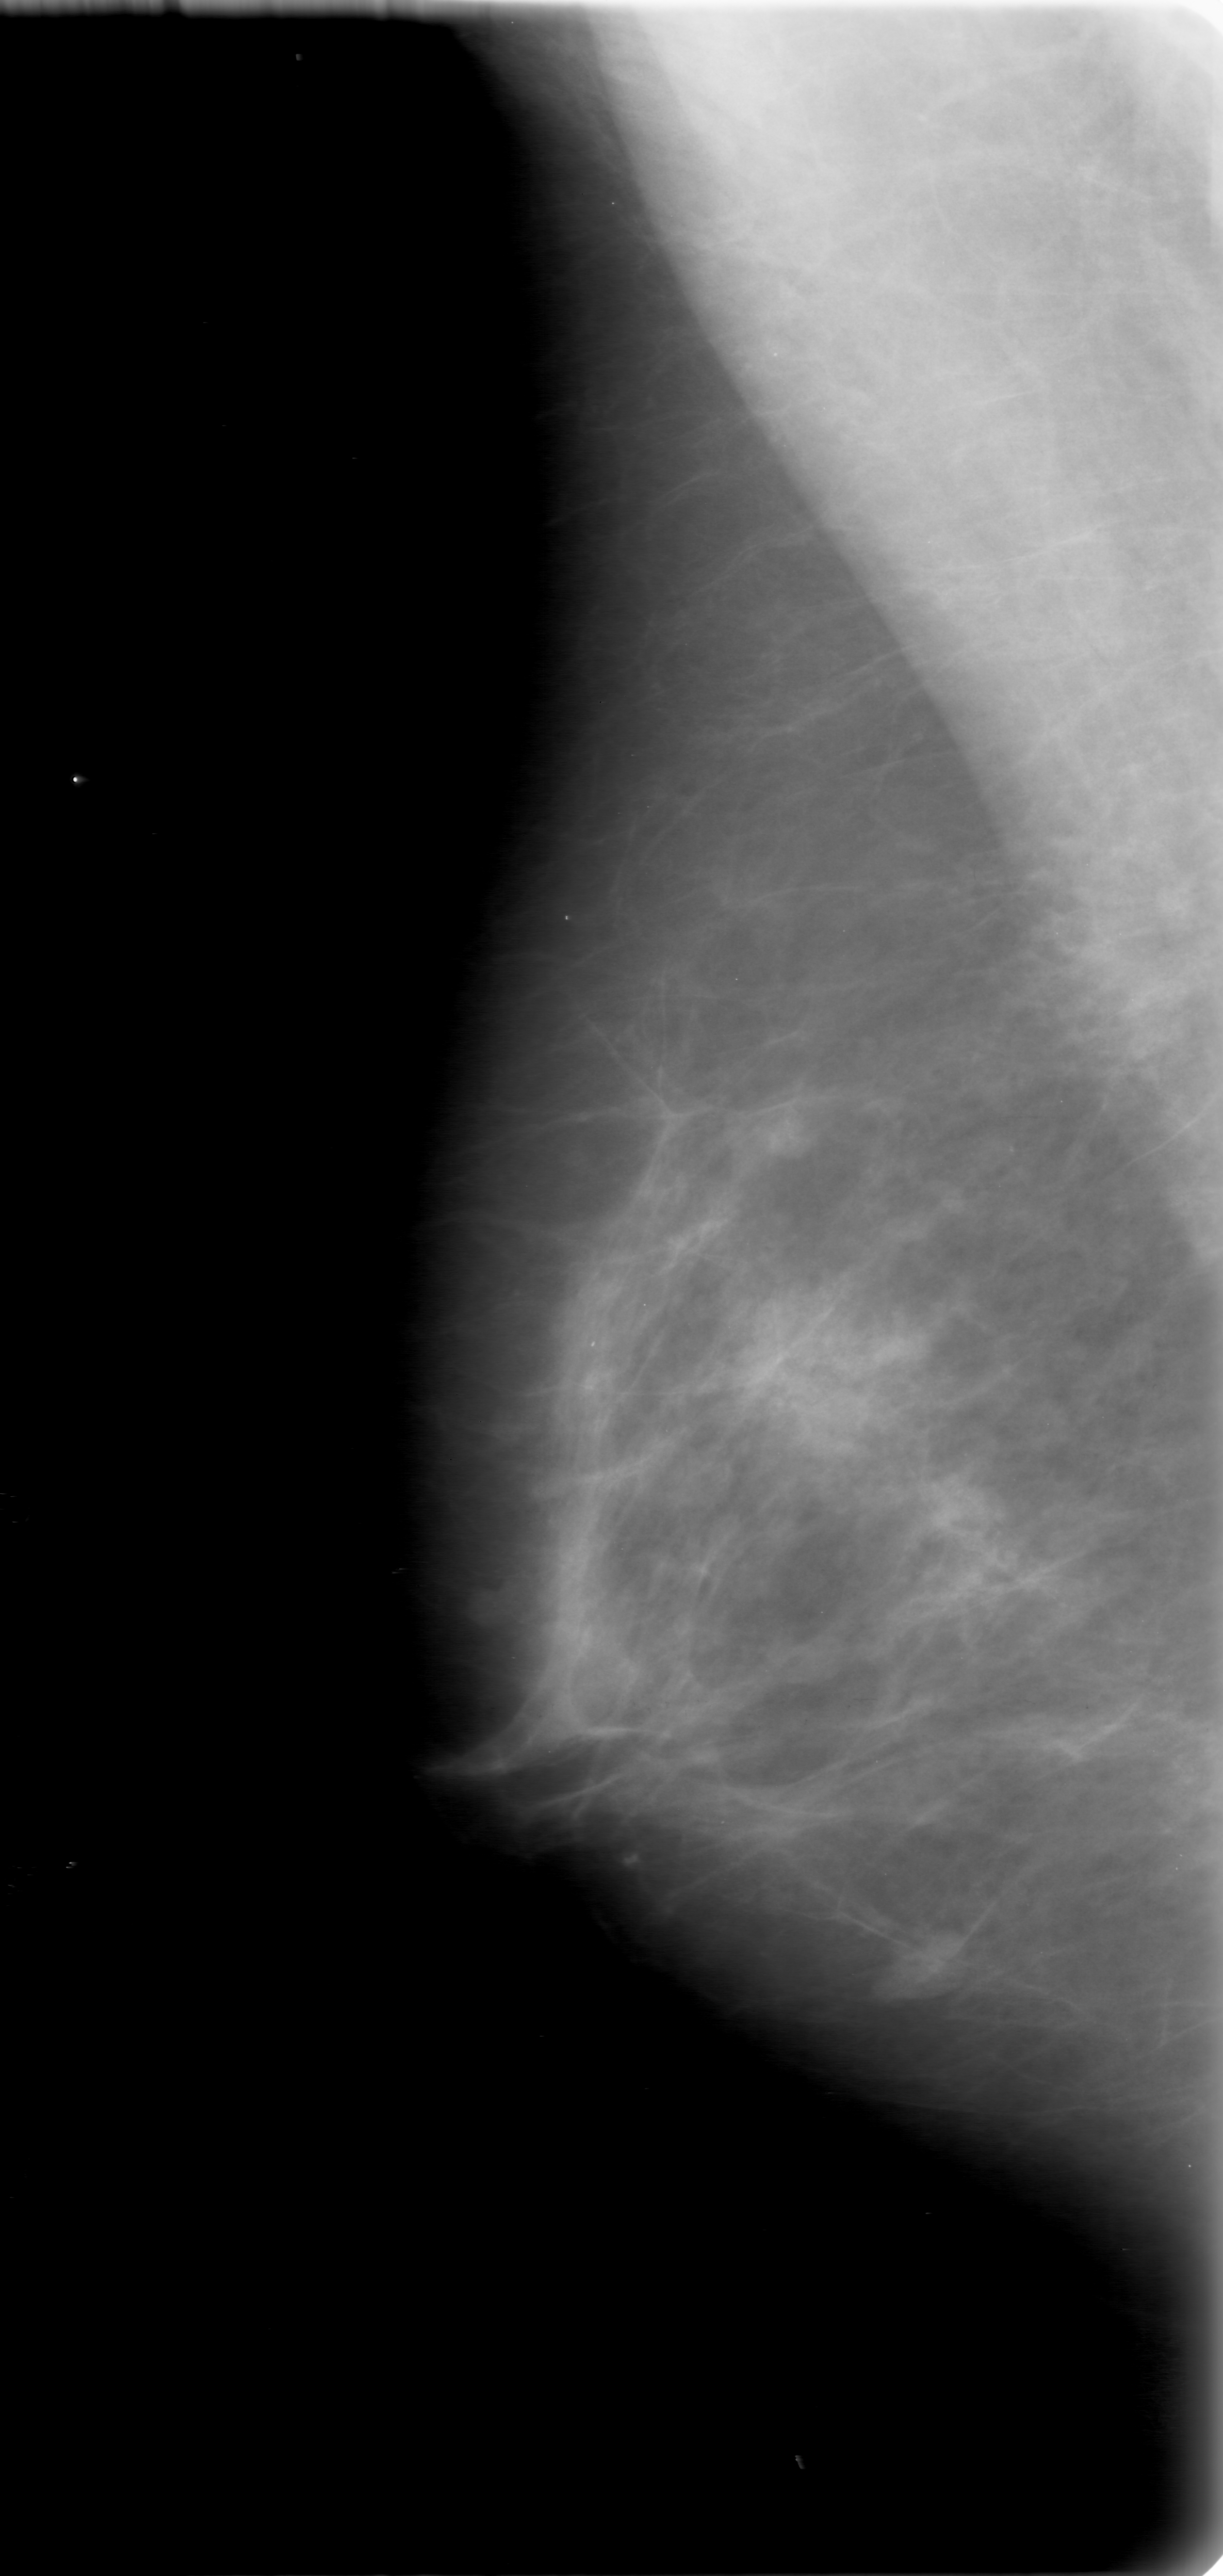
Mammogram (digitized film); right breast; mediolateral oblique (MLO) view; breast composition: scattered fibroglandular densities (BI-RADS density category 2 of 4).
- Finding: mass, shape oval, margins obscured; BI-RADS assessment category 0 (incomplete: needs additional imaging); subtlety rating 4 on a 1 (subtle) to 5 (obvious) scale; pathology (as recorded): benign.